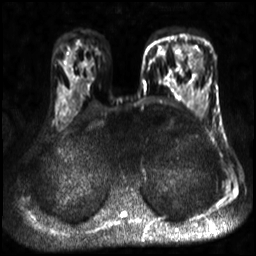
Breast MRI, one axial slice. Slice 17 of 30 in the series (ordered by position). Diffusion-weighted series; image 2 of 4 stored at this slice position (different b-values; order by instance number). 3 T. 4 mm slice thickness. 256 × 256 image matrix, field of view 320 × 320 mm. Female patient.
Outlined on this slice (outlined manually by an expert reader):
- tumour on diffusion-weighted imaging: bounding box [x1, y1, x2, y2] px = [183, 44, 204, 72]